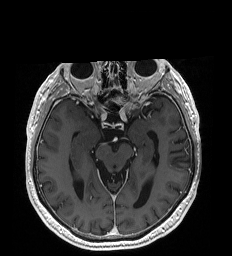
Brain MRI from a brain-tumour surgery series, one axial slice; position 119 of 192 along the scan axis; T1-weighted post-contrast; 1 mm slice thickness; 232 × 256 image matrix, field of view 227 × 250 mm. From the clinical record (not read from this slice): histopathology: Glioblastoma; WHO grade: 4; IDH mutation: no.
Outlined on this slice (expert manual segmentation):
- tumour: bounding box (x1, y1, x2, y2) in pixels: (117, 89, 130, 107)